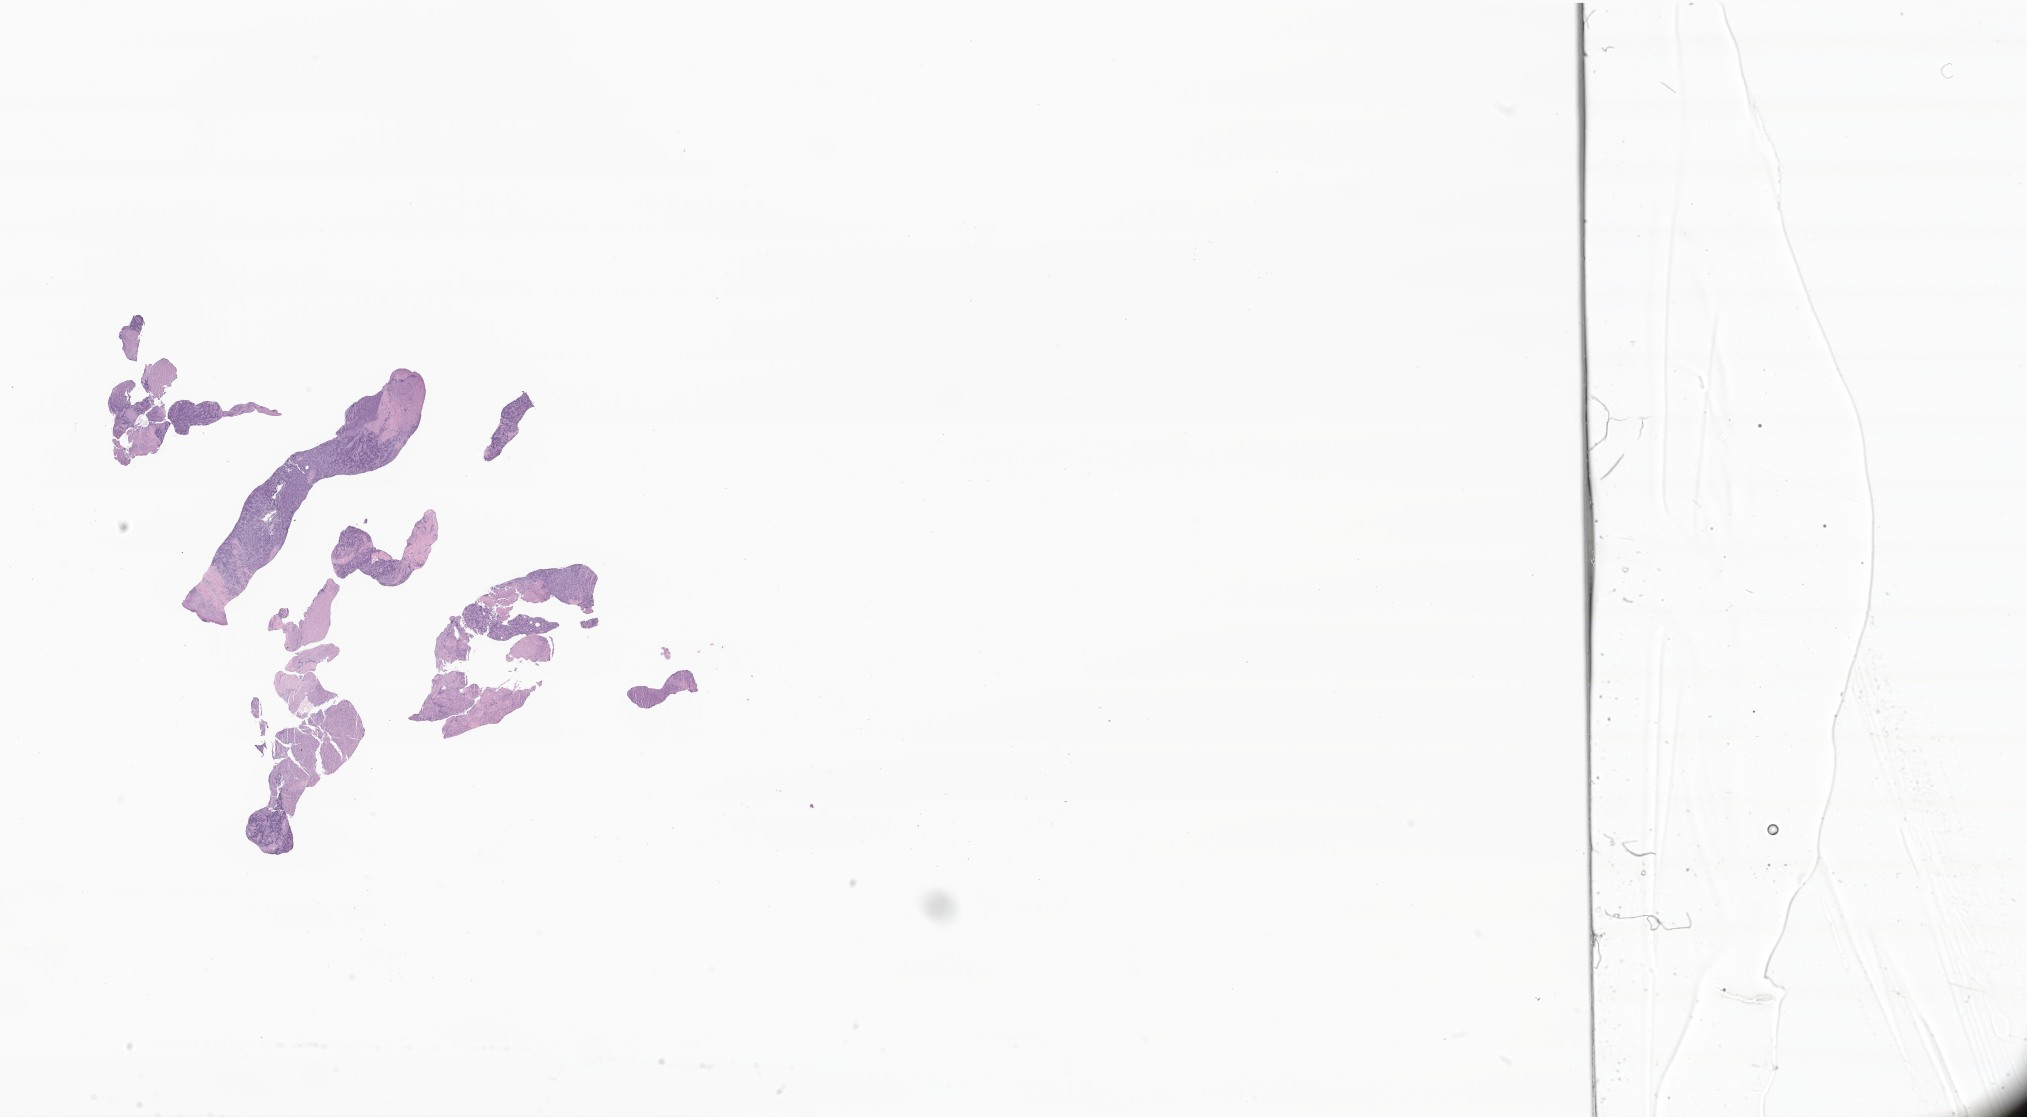
Whole-slide image, hematoxylin and eosin (H&E) stain of tumor tissue from the lower limb — a low-resolution overview of the entire scanned area, about 34.2 x 18.8 mm, formalin-fixed, paraffin-embedded (FFPE) tissue. Patient female; age 189 months (15 years 9 months).
Recorded diagnosis: Ewing sarcoma.